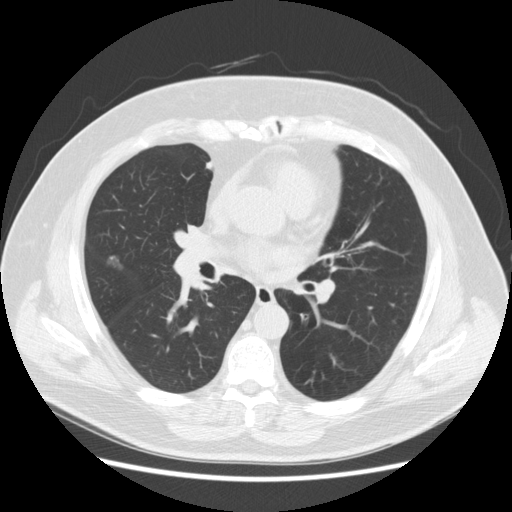
Axial slice from a low-dose chest CT screening exam. Baseline screening round. Lung window (W 1500 / L -600 HU). 2.5 mm slice thickness. Slice 106 of 213 in the series. 512 × 512 image matrix. Male participant, aged 67 years at enrolment. Former smoker at enrolment.
Lesion marked by an expert reader, bounding box [x1, y1, x2, y2] px = [96, 251, 128, 278]. Reader record for this screening exam (exam-level; its link to the box is not recorded): non-calcified nodule or mass ≥4 mm, right middle lobe, 15 × 11 mm, smooth margins, soft tissue attenuation. Official screen result: positive, change unspecified: nodule(s) >= 4 mm or enlarging nodule(s), mass(es), or other non-specific abnormalities suspicious for lung cancer. Later outcome: lung cancer diagnosed 409 days after this screen — adenocarcinoma, NOS, right middle lobe, moderately differentiated (G2), stage IA (AJCC 6th edition), 14 mm at pathology.